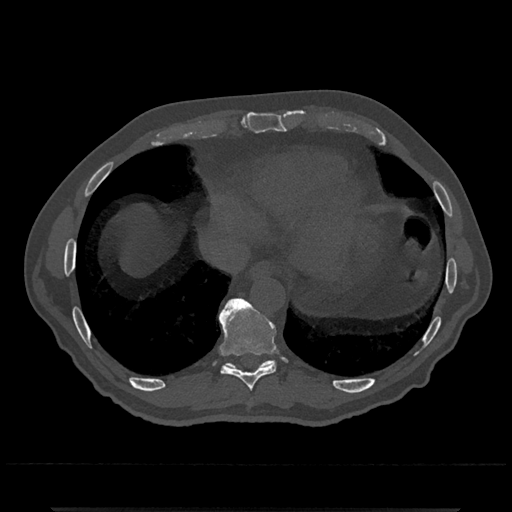
CT including the spine, one axial slice. Position 599 of 797 along the scan axis. Reconstruction kernel Br40s/3. Bone window (W 1800 / L 400 HU). 0.5 mm slice thickness. 512 × 512 image matrix, field of view 393 × 393 mm. Patient: male, 67 years. From the clinical record (not read from this slice): primary cancer: prostate.
Annotated regions visible in this slice (semi-automatically segmented with operator editing):
- T10 vertebra: bounding box (x1, y1, x2, y2) in pixels: (225, 298, 275, 367)
- T9 vertebra: (219, 298, 277, 391)